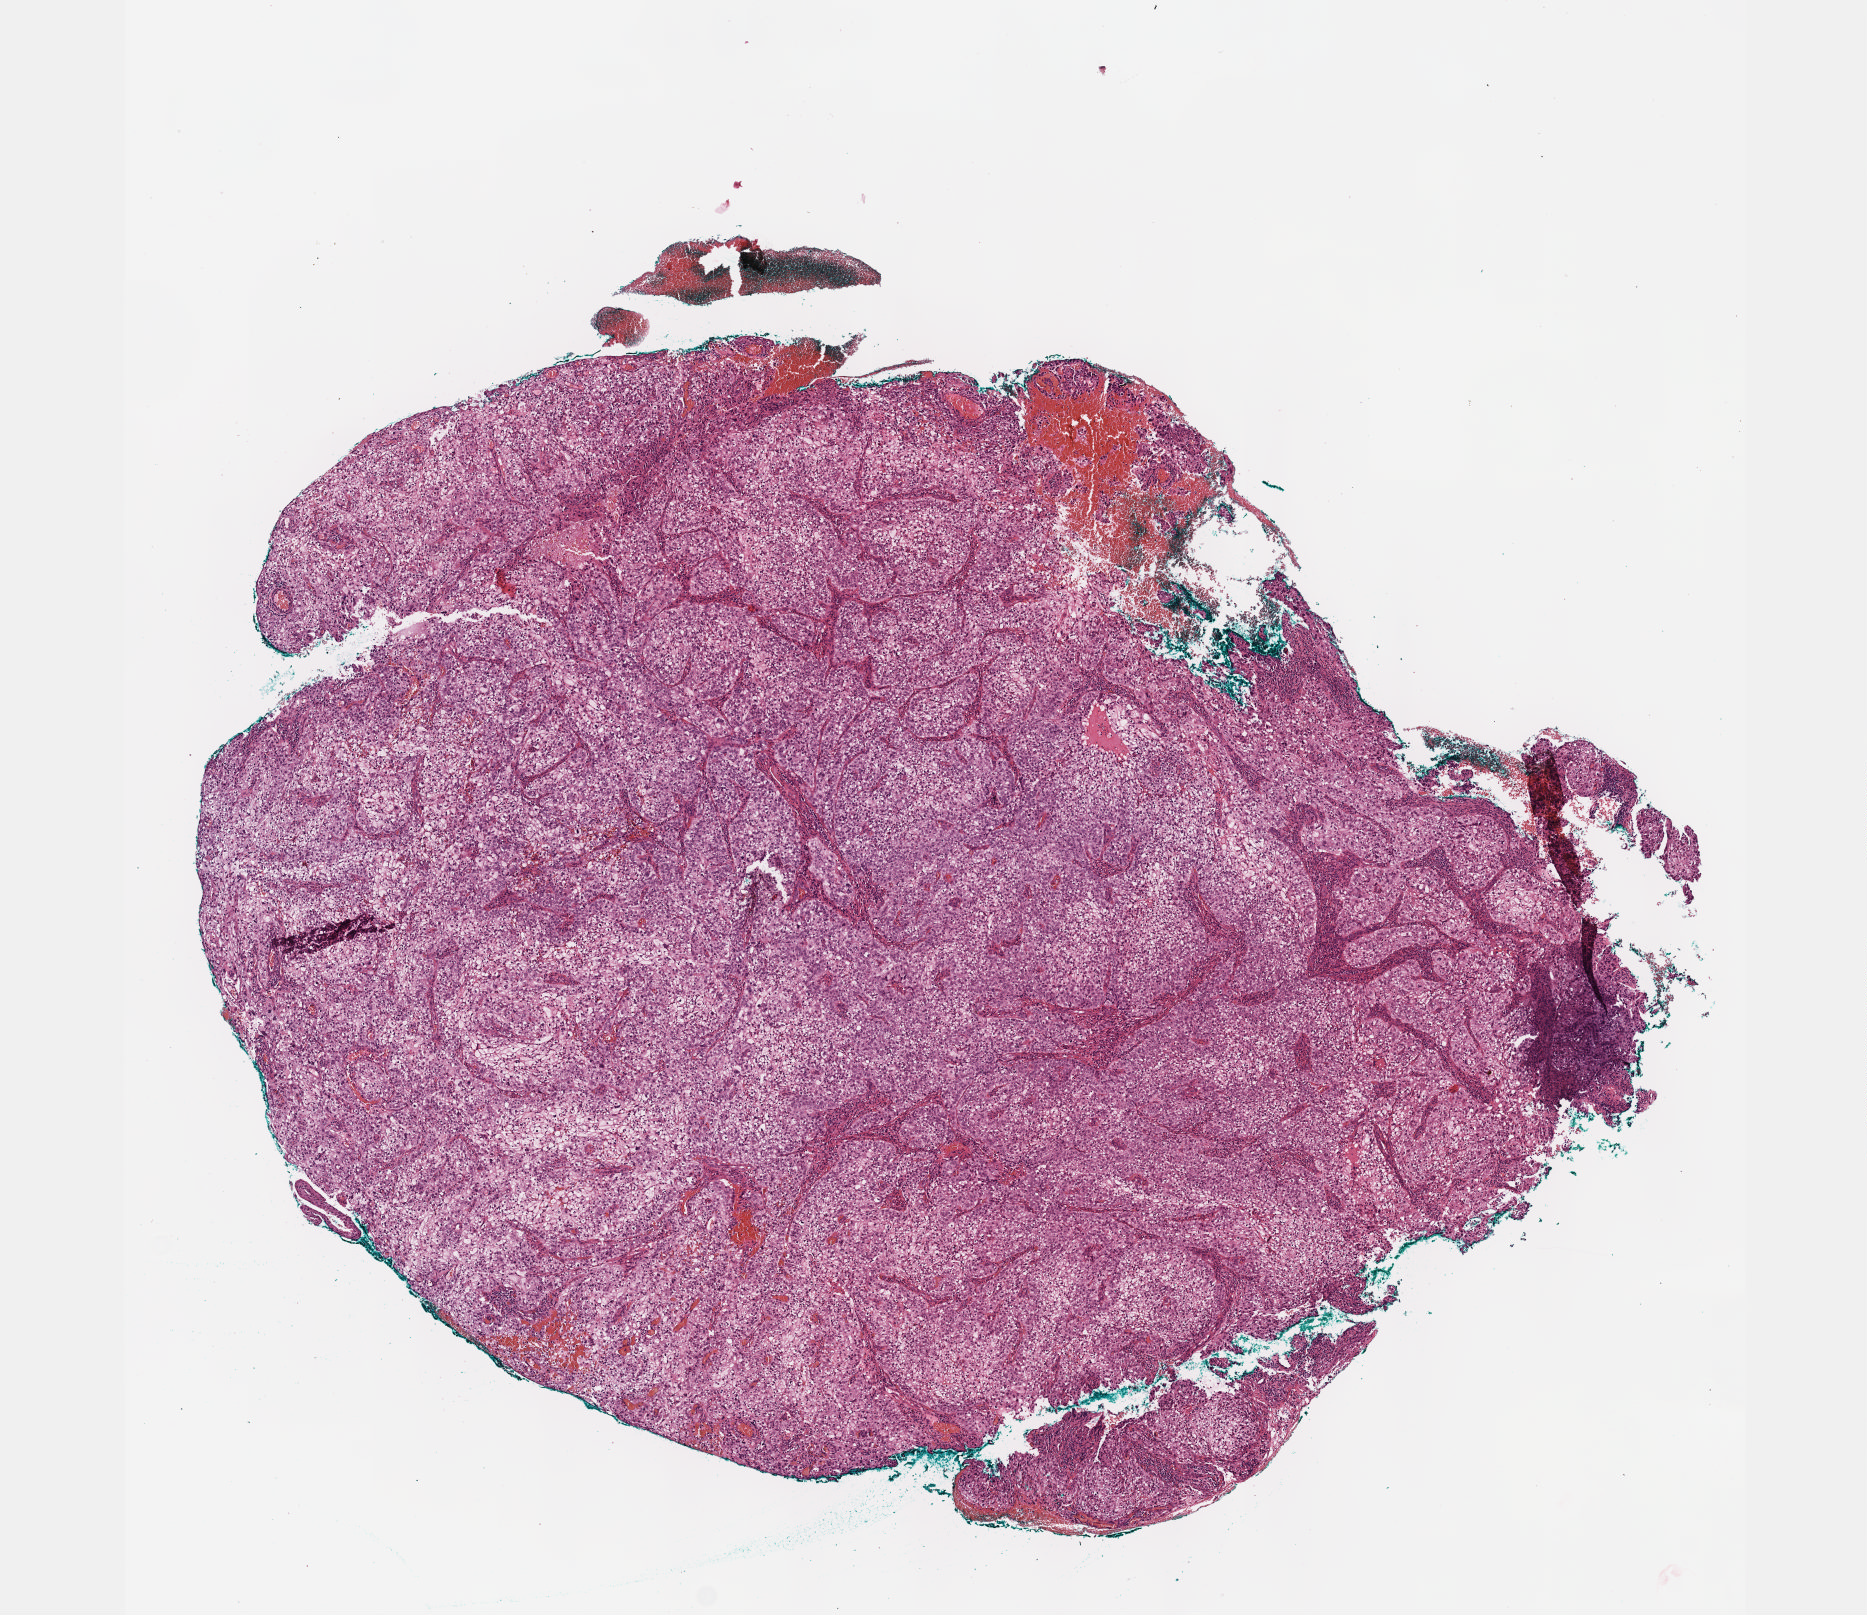
H&E-stained whole-slide image, low-resolution overview of the scanned area, about 7.5 x 6.5 mm, formalin-fixed paraffin-embedded (FFPE) diagnostic section, primary tumour sample from the cervix. Female, age 79 years at initial diagnosis.
Pathologic diagnosis: Squamous cell carcinoma, NOS.